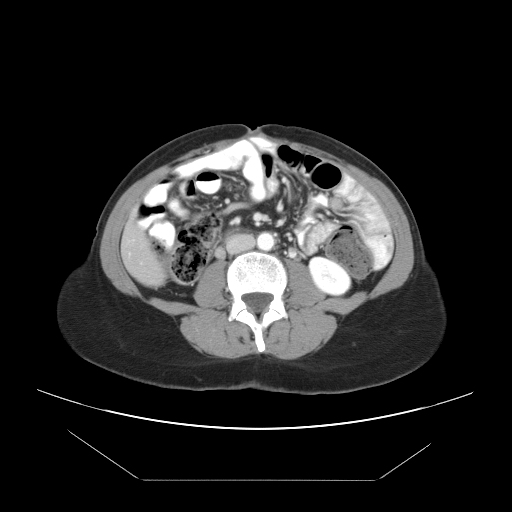
Contrast-enhanced abdominal CT, one axial slice. Slice 8 of 45 in the series (ordered by position). Reconstruction kernel STANDARD. Intravenous contrast given. Soft-tissue window (W 400 / L 40 HU). 5 mm slice thickness. 512 × 512 image matrix, field of view 405 × 405 mm. Female patient, age 52 years. Case-level facts recorded for this patient, not image findings: diagnosis: colorectal cancer liver metastases, imaged before liver resection; multiple liver metastases: yes; largest metastasis: 2.5 cm; chemotherapy before resection: yes.
Outlined on this slice (outlined manually by an expert reader):
- liver: box from (x=124, y=225) to (x=161, y=285) px
- planned liver remnant (the part of the liver to remain after resection): (x=124, y=225)–(x=153, y=261)